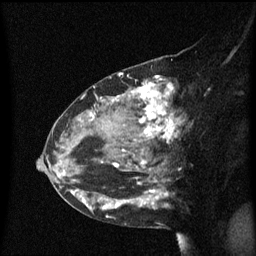
Breast MRI (dynamic contrast-enhanced), one sagittal slice; position 35 of 60 along the scan axis; dynamic contrast-enhanced series, image 2 of 3 at this slice position (ordered by acquisition); 1.5 T; TE 4.2 ms, TR 8.4 ms; 2 mm slice thickness; 256 × 256 image matrix. Female patient, age 48 years. Case-level facts recorded for this patient, not image findings: setting: breast cancer imaged before/during neoadjuvant chemotherapy; receptor status: HR-positive, HER2-negative.
Structures marked on this image (semi-automatically segmented with operator editing):
- analysis volume of interest (the breast-tissue region the enhancement analysis was run in; not a lesion): bounding box [x1, y1, x2, y2] px = [80, 78, 187, 221]
- tumour enhancement mask (voxels above the 70 % enhancement threshold inside the analysis volume of interest): [90, 78, 179, 212]